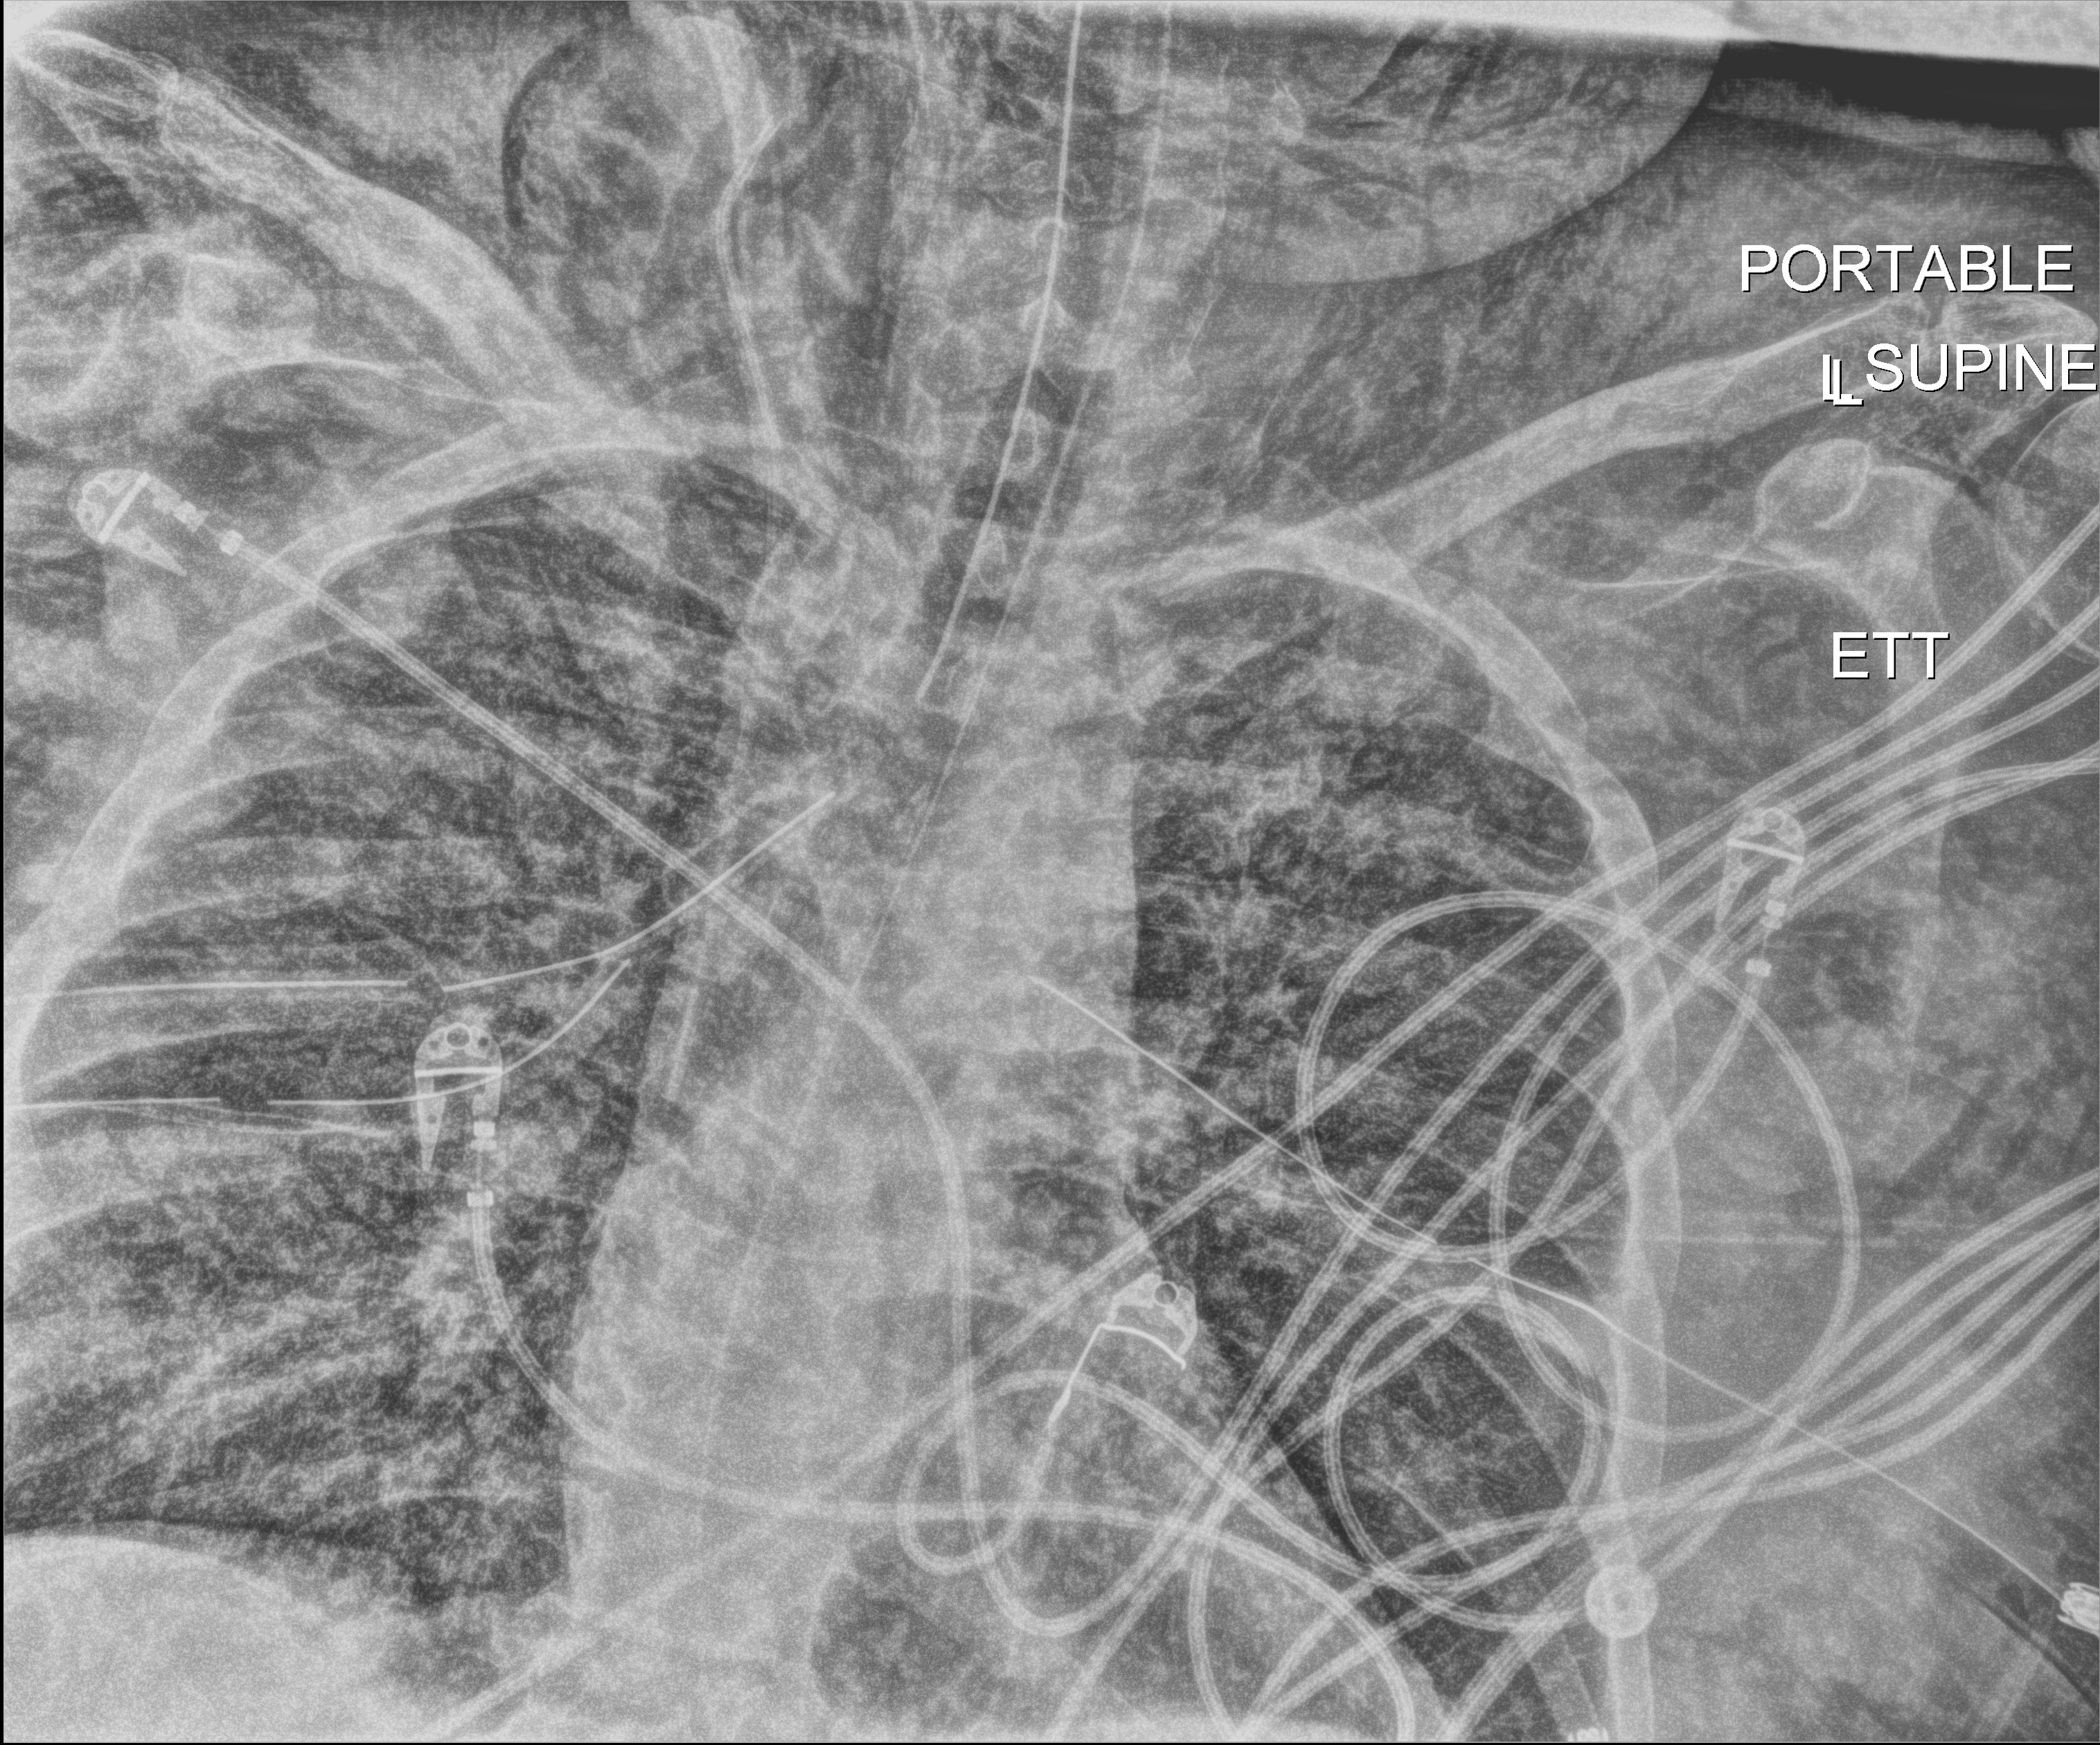
Portable chest radiograph, anteroposterior (AP) projection. Adult patient hospitalised with COVID-19, age 18–59 years.
Admission-level facts for this patient (not findings on this image; timing relative to this image not recorded): diabetes (admission record): yes; hypertension (admission record): yes.